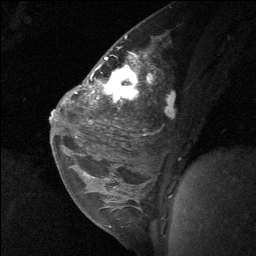
Breast MRI (dynamic contrast-enhanced), one sagittal slice; slice 39 of 64 in the series (ordered by position); dynamic contrast-enhanced study with each time point stored as its own series, time point 2 of 3 at this slice position (early post-contrast, ordered by acquisition time); 1.5 T; TE 4.8 ms, TR 27 ms; 256 × 256 image matrix. Patient: female, 26 years. From the clinical record (not read from this slice): setting: breast cancer imaged before/during neoadjuvant chemotherapy; receptor status: HR-positive, HER2-negative.
Outlined on this slice (semi-automatically segmented with operator editing):
- analysis volume of interest (the breast-tissue region the enhancement analysis was run in; not a lesion): bounding box [x1, y1, x2, y2] px = [86, 43, 149, 138]
- tumour enhancement mask (voxels above the 90 % enhancement threshold inside the analysis volume of interest): [90, 56, 139, 103]